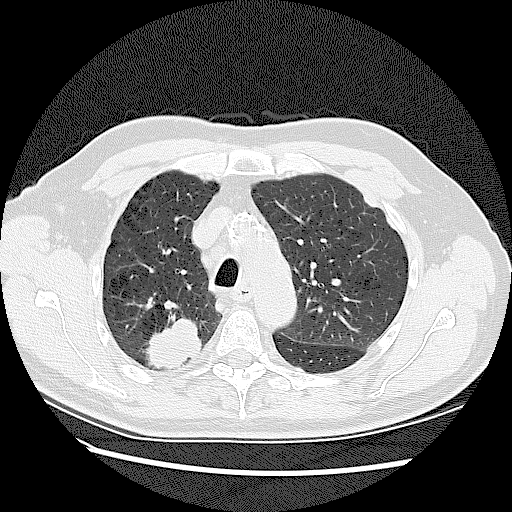
Chest CT (low-dose screening protocol), one axial image. Baseline screening round. Lung window (W 1500 / L -600 HU). 2.5 mm slice thickness. 120 kVp. Slice 36 of 128 in the series. Male participant, aged 72 years at enrolment. Current smoker at enrolment.
Expert reader's lesion annotation, bounding box [x1, y1, x2, y2] px = [138, 311, 213, 376]. The screening reader recorded 2 non-calcified nodules or masses ≥4 mm on this exam; which of them this box marks is not recorded. Participant outcome: lung cancer diagnosed 42 days after this screen — adenocarcinoma, NOS, right upper lobe, stage IV (AJCC 6th edition), 45 mm at pathology.